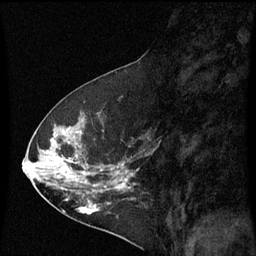
Breast MRI (dynamic contrast-enhanced), one sagittal slice. Position 28 of 60 along the scan axis. Dynamic contrast-enhanced series, image 2 of 3 at this slice position (ordered by acquisition). 1.5 T. TE 4.2 ms, TR 8.9 ms. 2 mm slice thickness. 256 × 256 image matrix, field of view 200 × 200 mm. Female patient, age 53 years. Case-level facts recorded for this patient, not image findings: setting: breast cancer imaged before/during neoadjuvant chemotherapy; receptor status: HR-positive, HER2-negative.
Structures marked on this image (semi-automatic segmentation, software-assisted and operator-edited):
- analysis volume of interest (the breast-tissue region the enhancement analysis was run in; not a lesion): bounding box (x1, y1, x2, y2) in pixels: (32, 100, 145, 221)
- tumour enhancement mask (voxels above the 70 % enhancement threshold inside the analysis volume of interest): (52, 132, 129, 215)